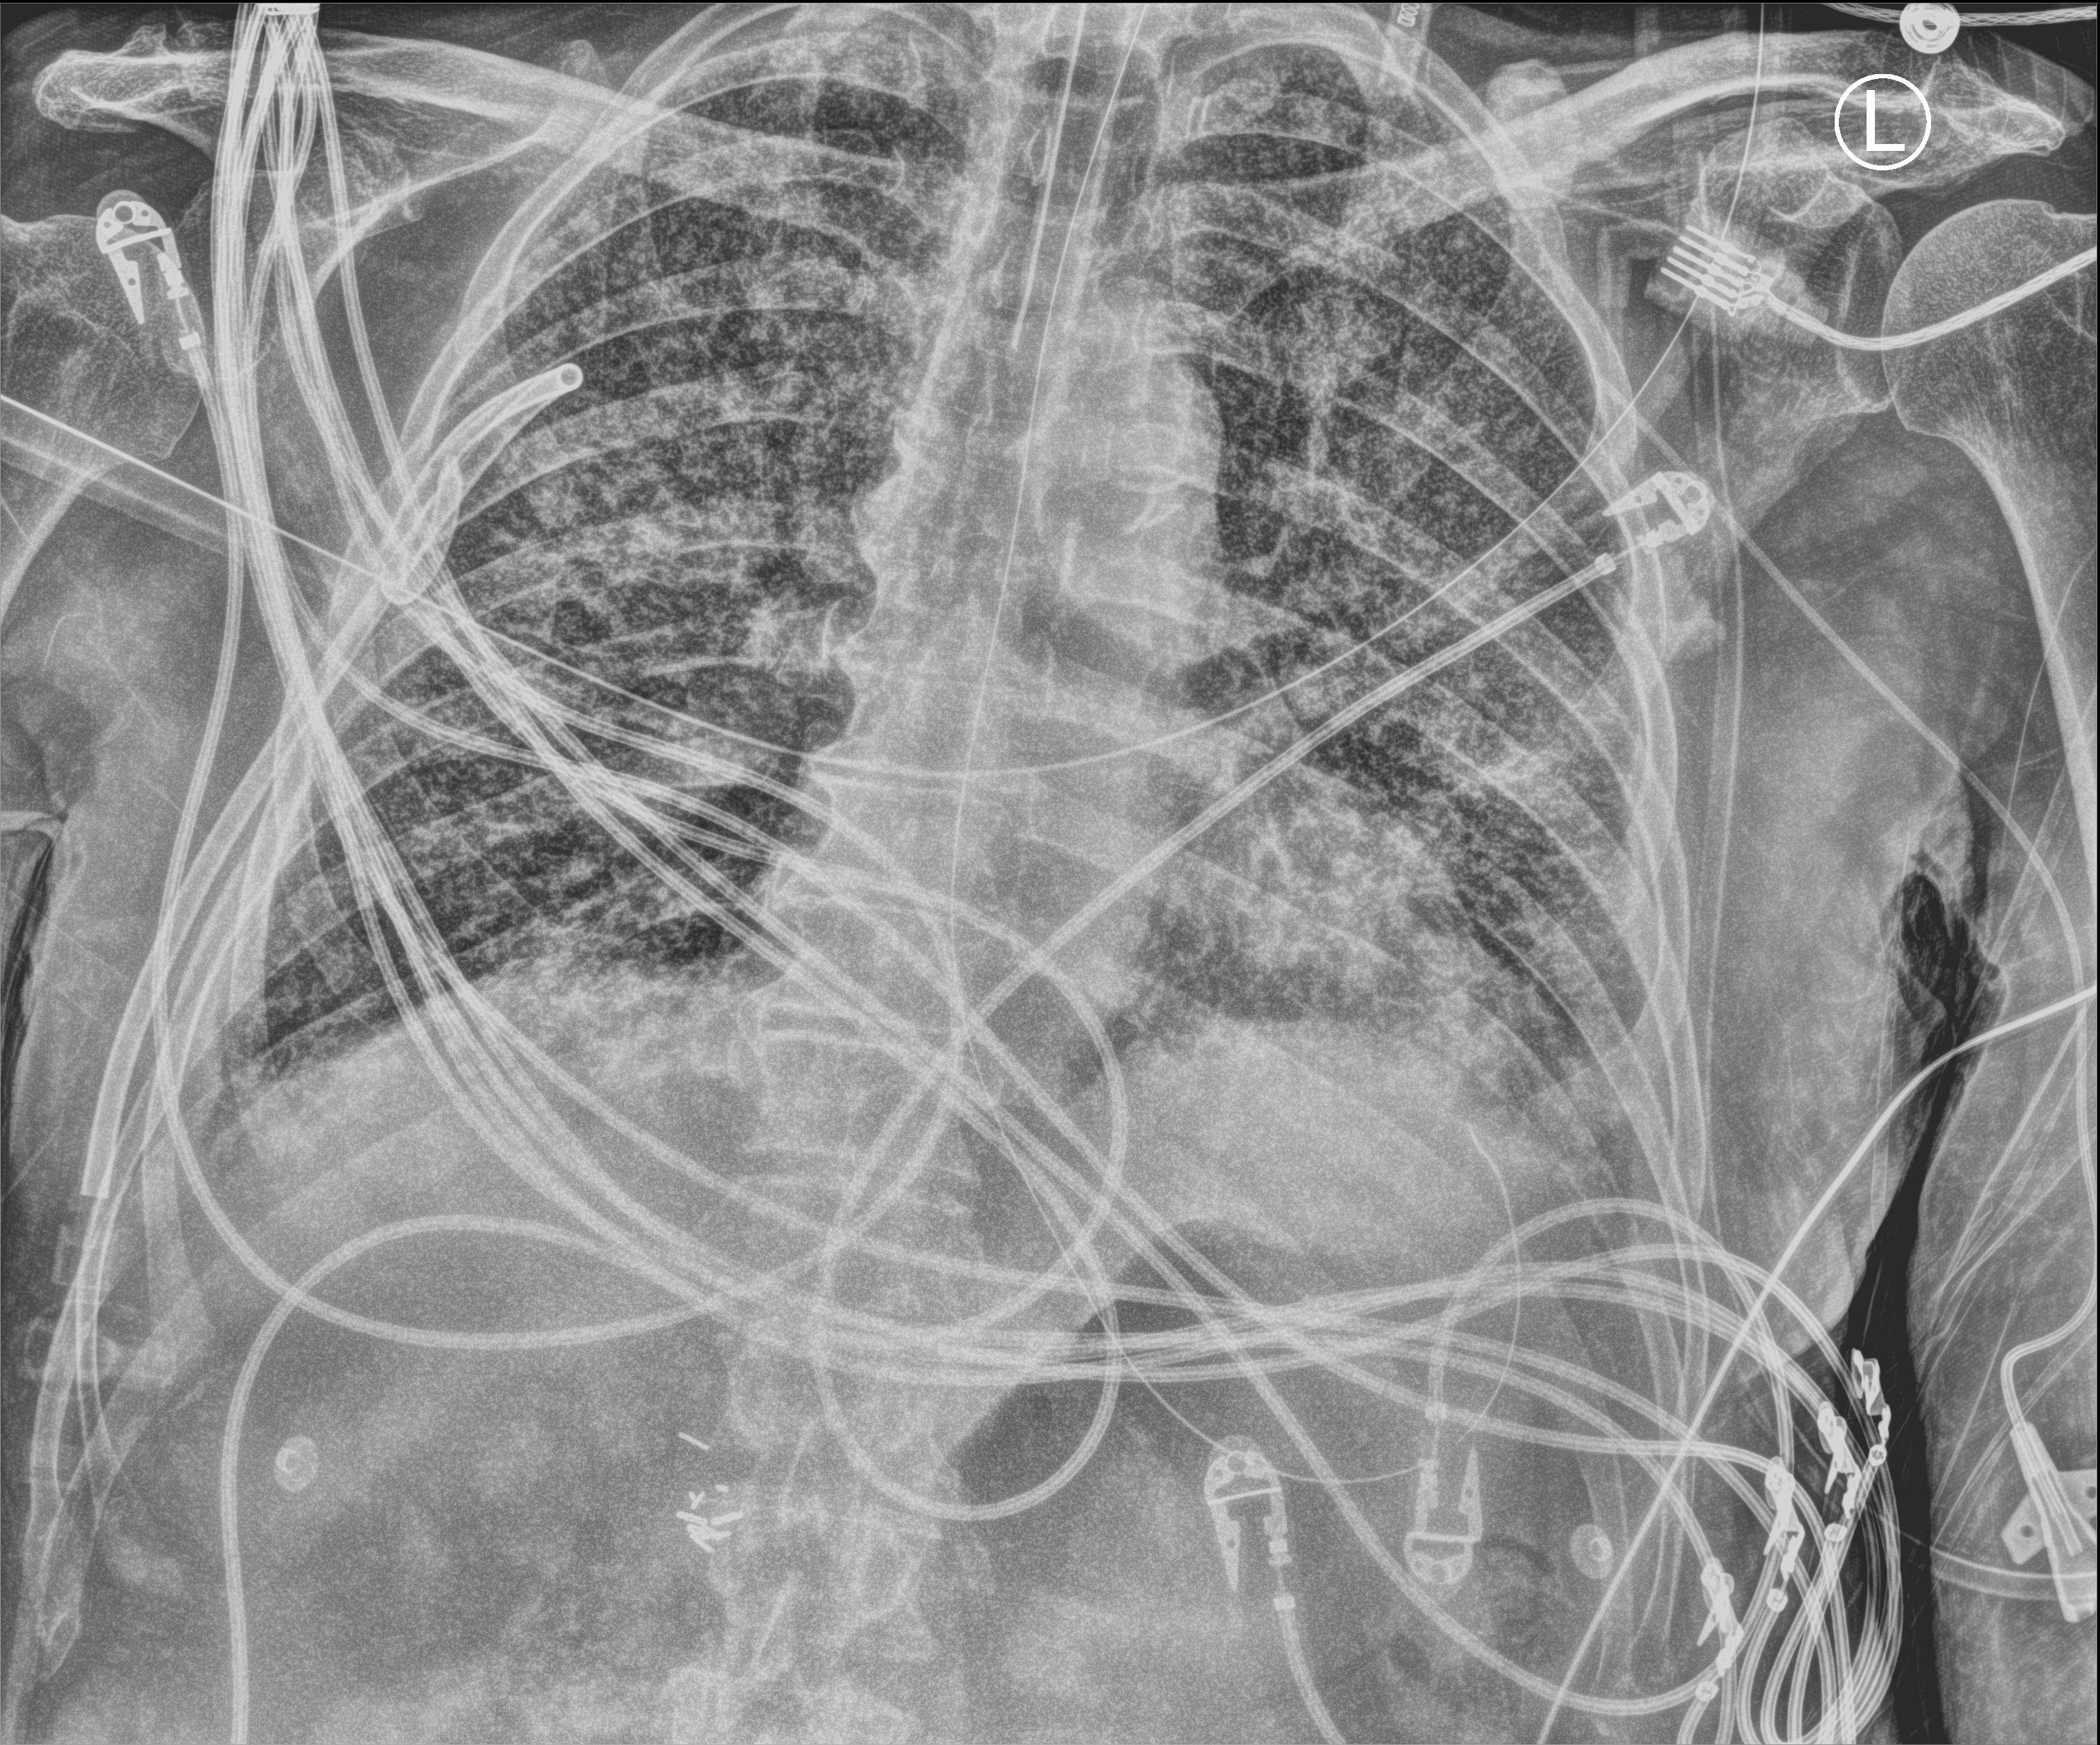
Portable chest radiograph; anteroposterior (AP) projection. Male patient hospitalised with COVID-19, age 75–90 years.
From the hospital-stay record, not from the radiograph (when in the stay this image was taken is not recorded): other chronic lung disease (admission record): no.